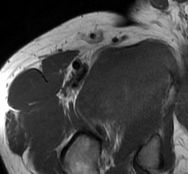
MRI of an extremity soft-tissue mass, one axial slice; slice 67 of 93 in the series (ordered by position); MR volume resampled by the dataset authors to the PET/CT grid (not the native acquisition matrix); 3.27 mm slice thickness; 188 × 174 image matrix. Male patient. Case-level facts recorded for this patient, not image findings: histological type: undifferentiated - pleiomorphic; grade: high; site of the primary tumour: right thigh.
Outlined on this slice (expert contour drawn on MRI and transferred to this co-registered scan by the dataset authors):
- gross tumour volume including surrounding oedema: bounding box (x1, y1, x2, y2) in pixels: (97, 42, 176, 127)
- gross tumour volume (mass): (97, 49, 176, 125)